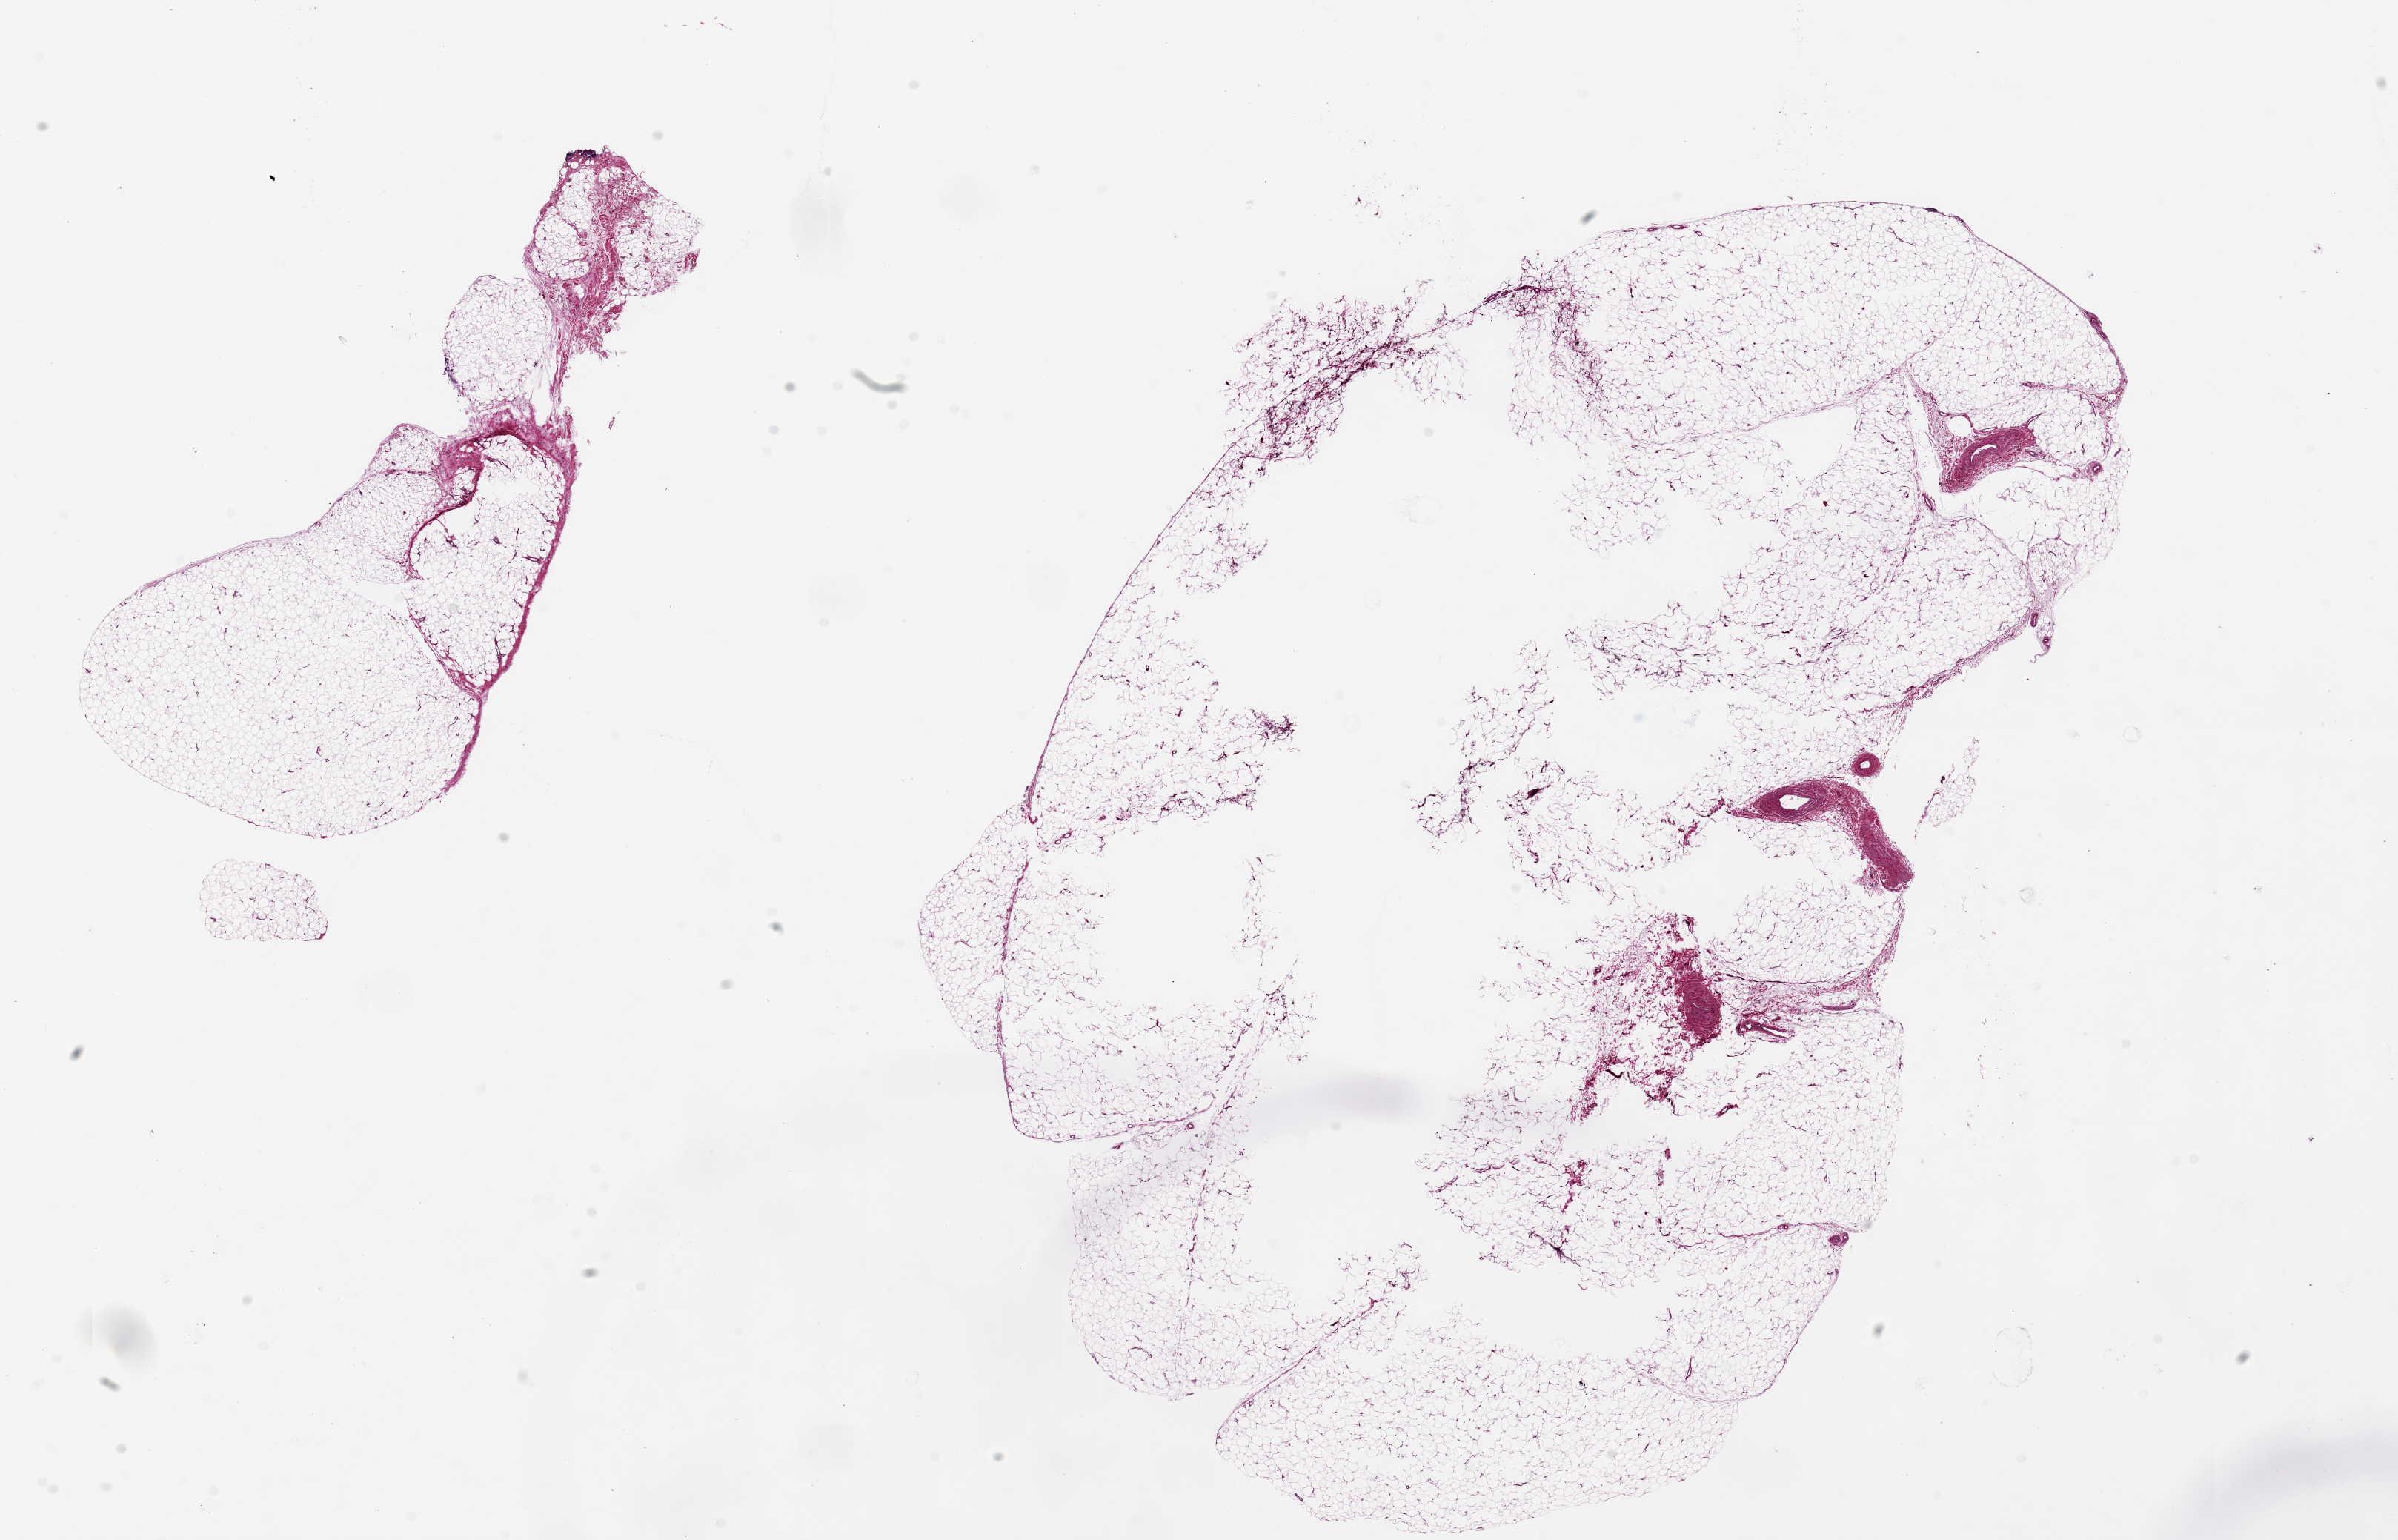
Whole-slide image, hematoxylin and eosin (H&E) stain — a low-resolution overview of the entire scanned area, about 25.6 x 16.4 mm; PAXgene-fixed paraffin-embedded (PFPE) section; target tissue: adipose tissue; tissue donor sample.
• review note (as recorded): 2 pieces, 15x11 & 9x4mm; large piece has 10x5mm central fixation defect